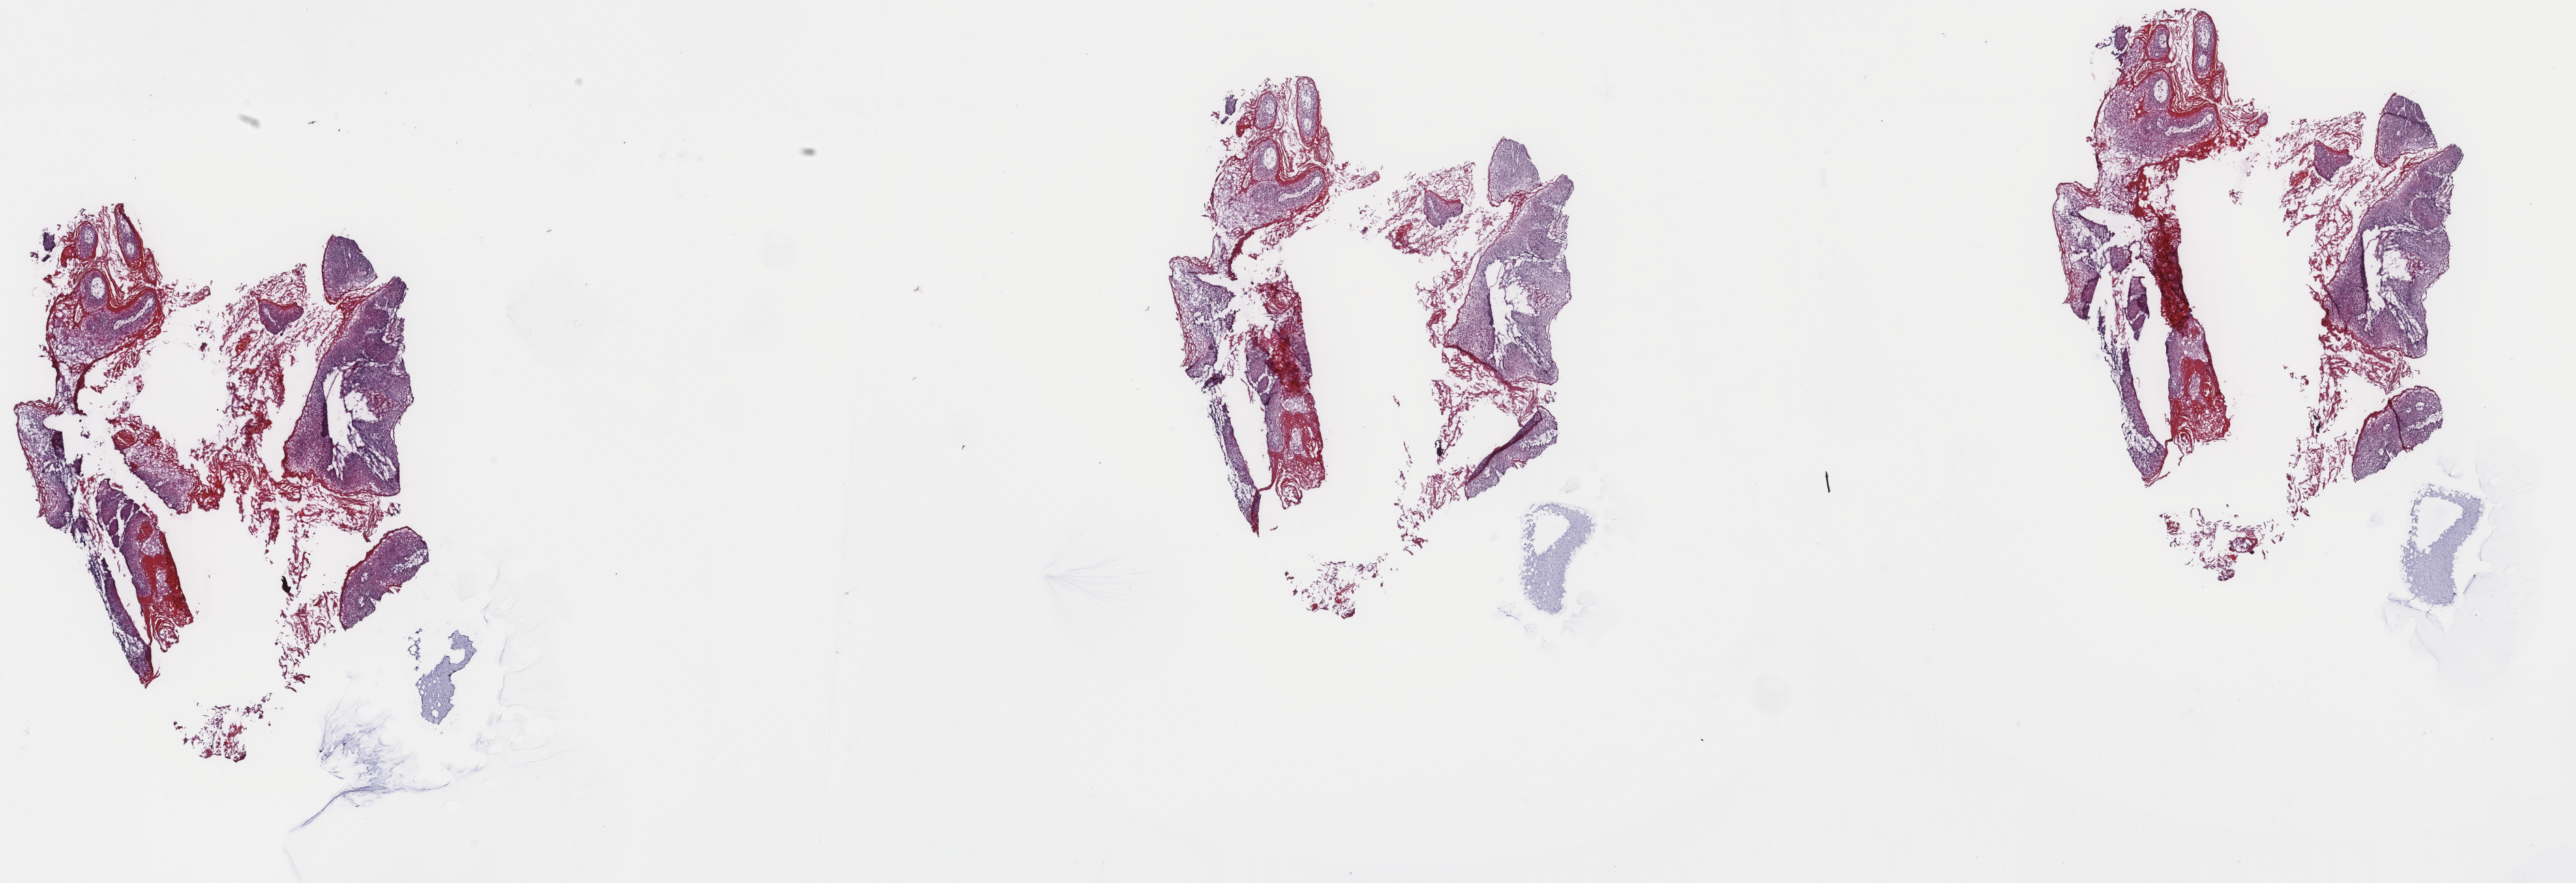
Digitized H&E-stained tissue section (whole slide), a low-resolution overview of the entire scanned area, about 30.0 x 10.3 mm (slide scanned at 40x); frozen section from the top of the tissue portion; sample: primary tumour, head and neck. Female patient; age at initial diagnosis 82 years. Histologic grade: G2 (moderately differentiated). Slide review estimates, as recorded: tumour cells 80%, tumour nuclei 90%, normal cells 0%, stromal cells 5%, necrosis 15%. Inflammatory infiltration, as recorded: lymphocyte infiltration 0%, monocyte infiltration 0%, neutrophil infiltration 0%.
AJCC pathologic stage: IVA (6th edition). Pathologic diagnosis: Squamous cell carcinoma, NOS (floor of mouth, NOS).